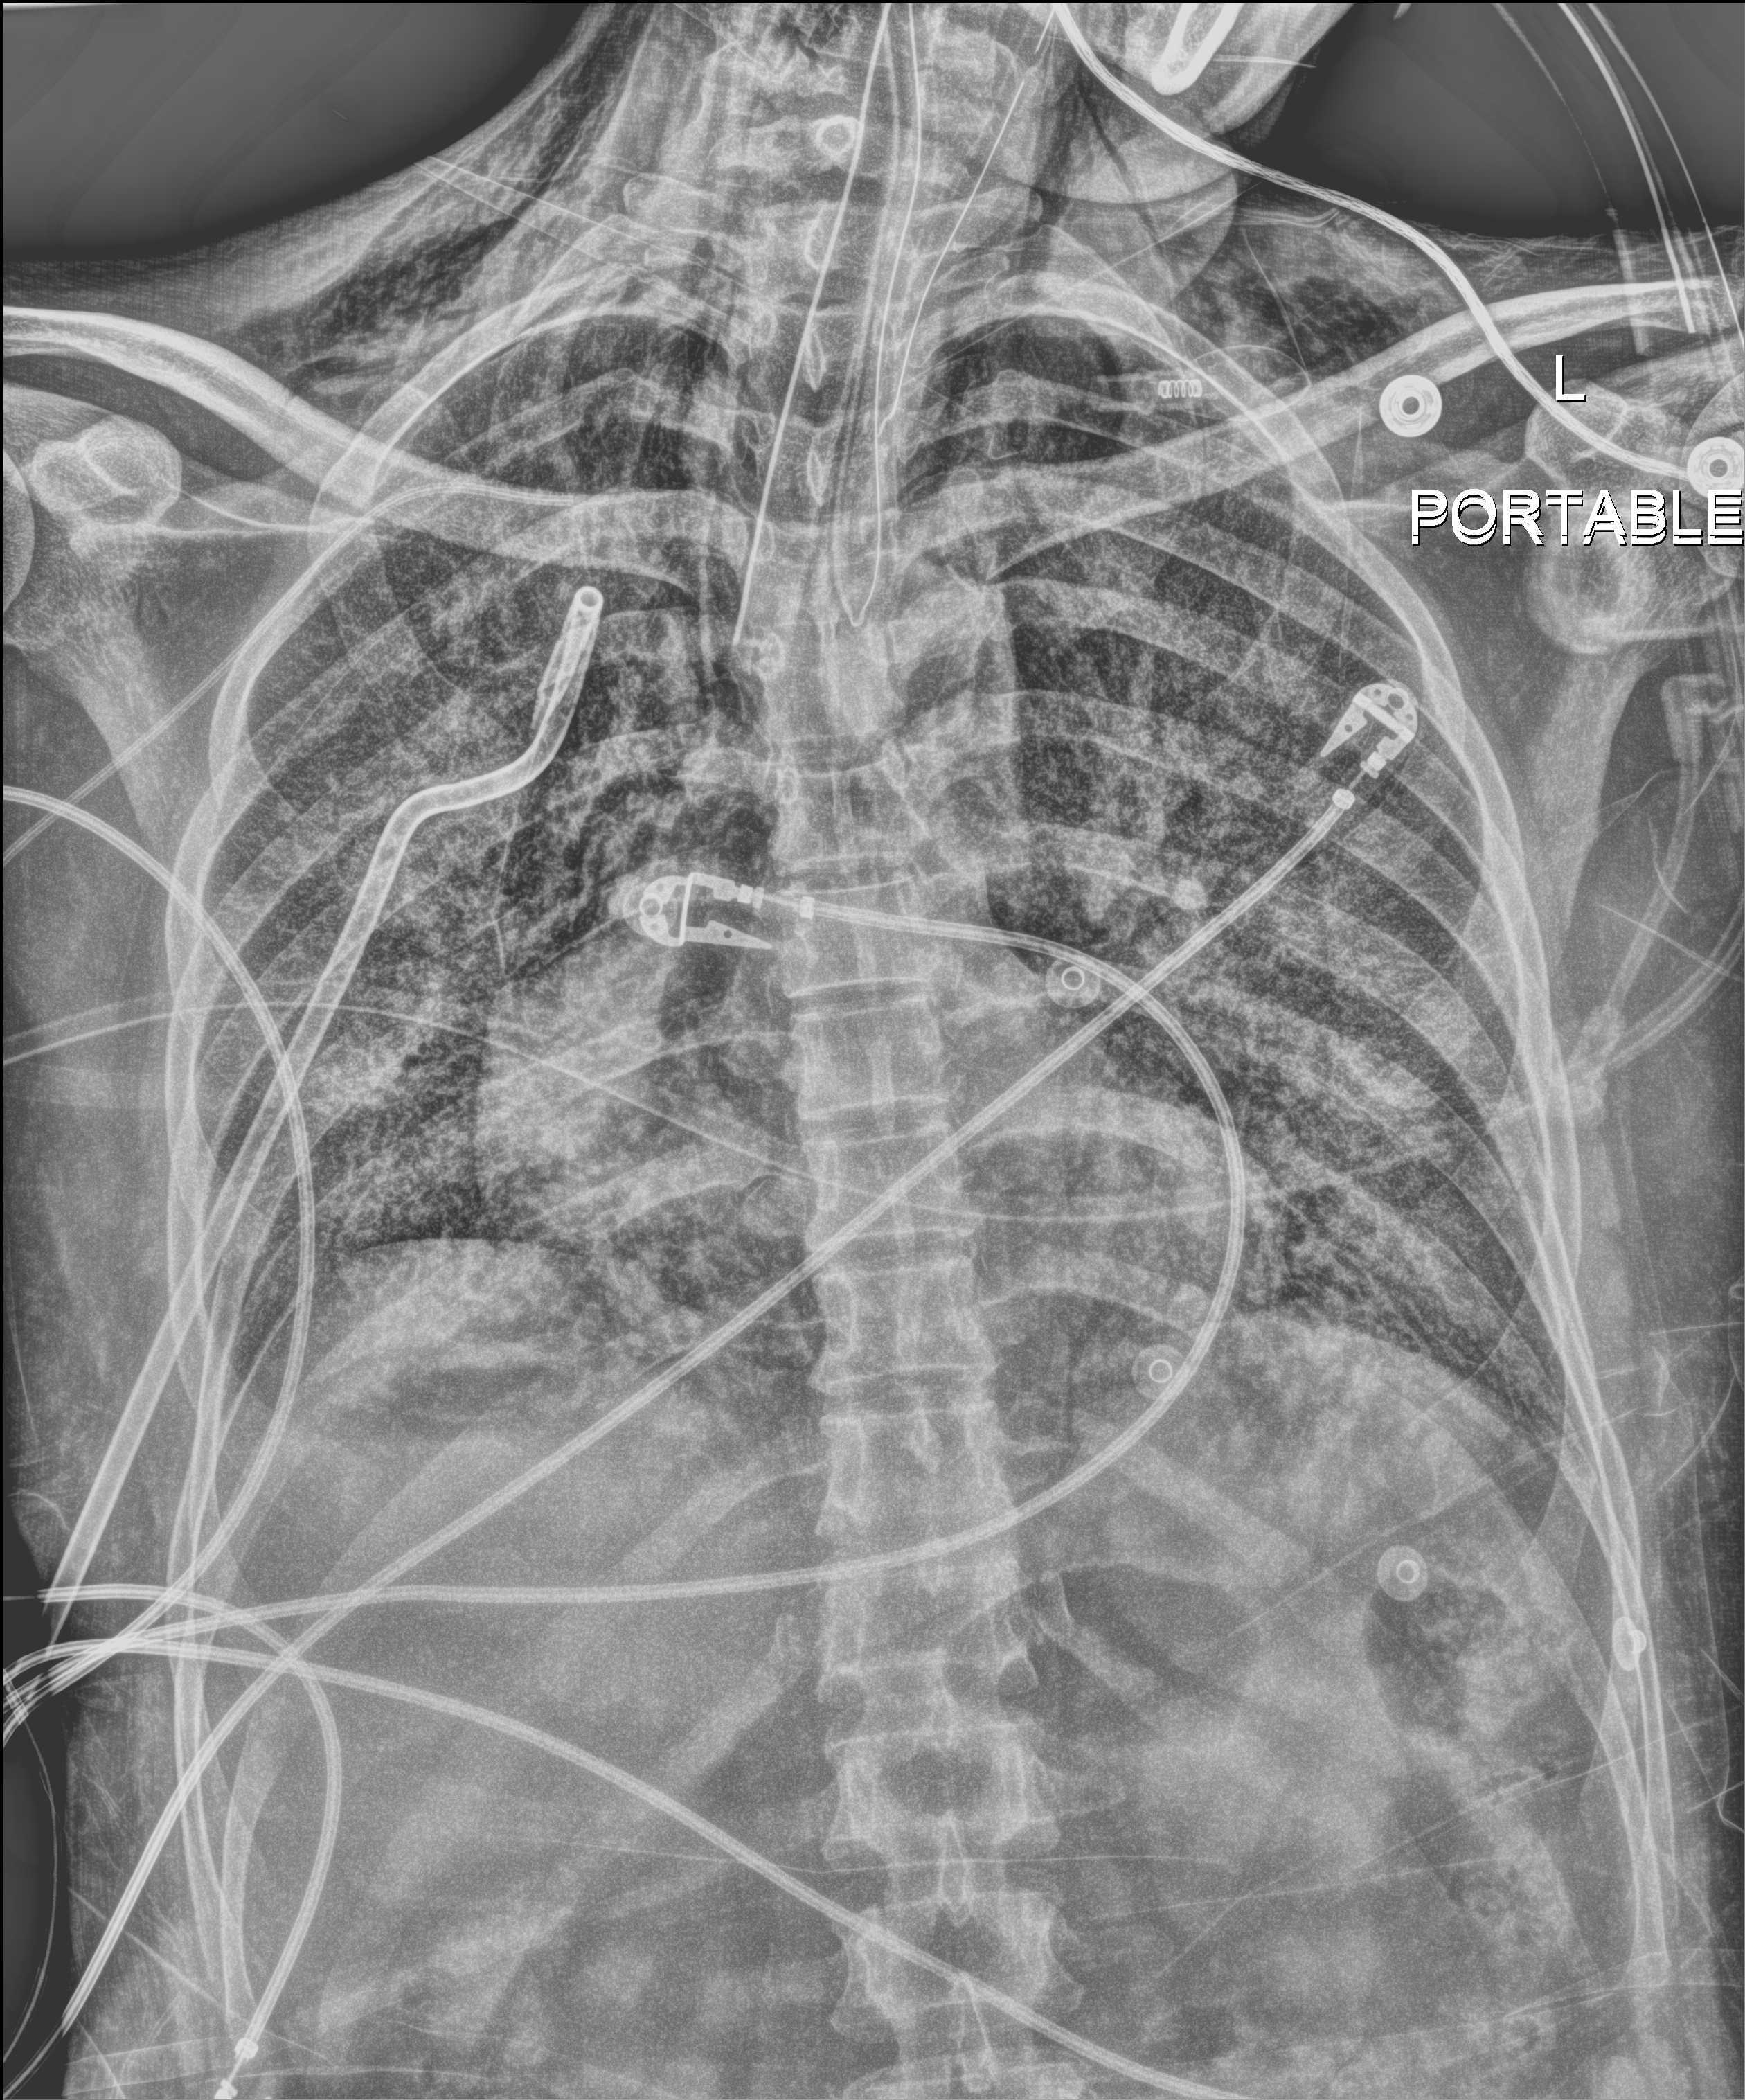
Chest X-ray (portable); anteroposterior (AP) projection. Patient hospitalised with COVID-19, aged 18–59 years.
From the hospital-stay record, not from the radiograph (when in the stay this image was taken is not recorded):
- hypertension (admission record): no
- admitted to intensive care during this hospital stay: yes
- length of hospital stay: 41 days